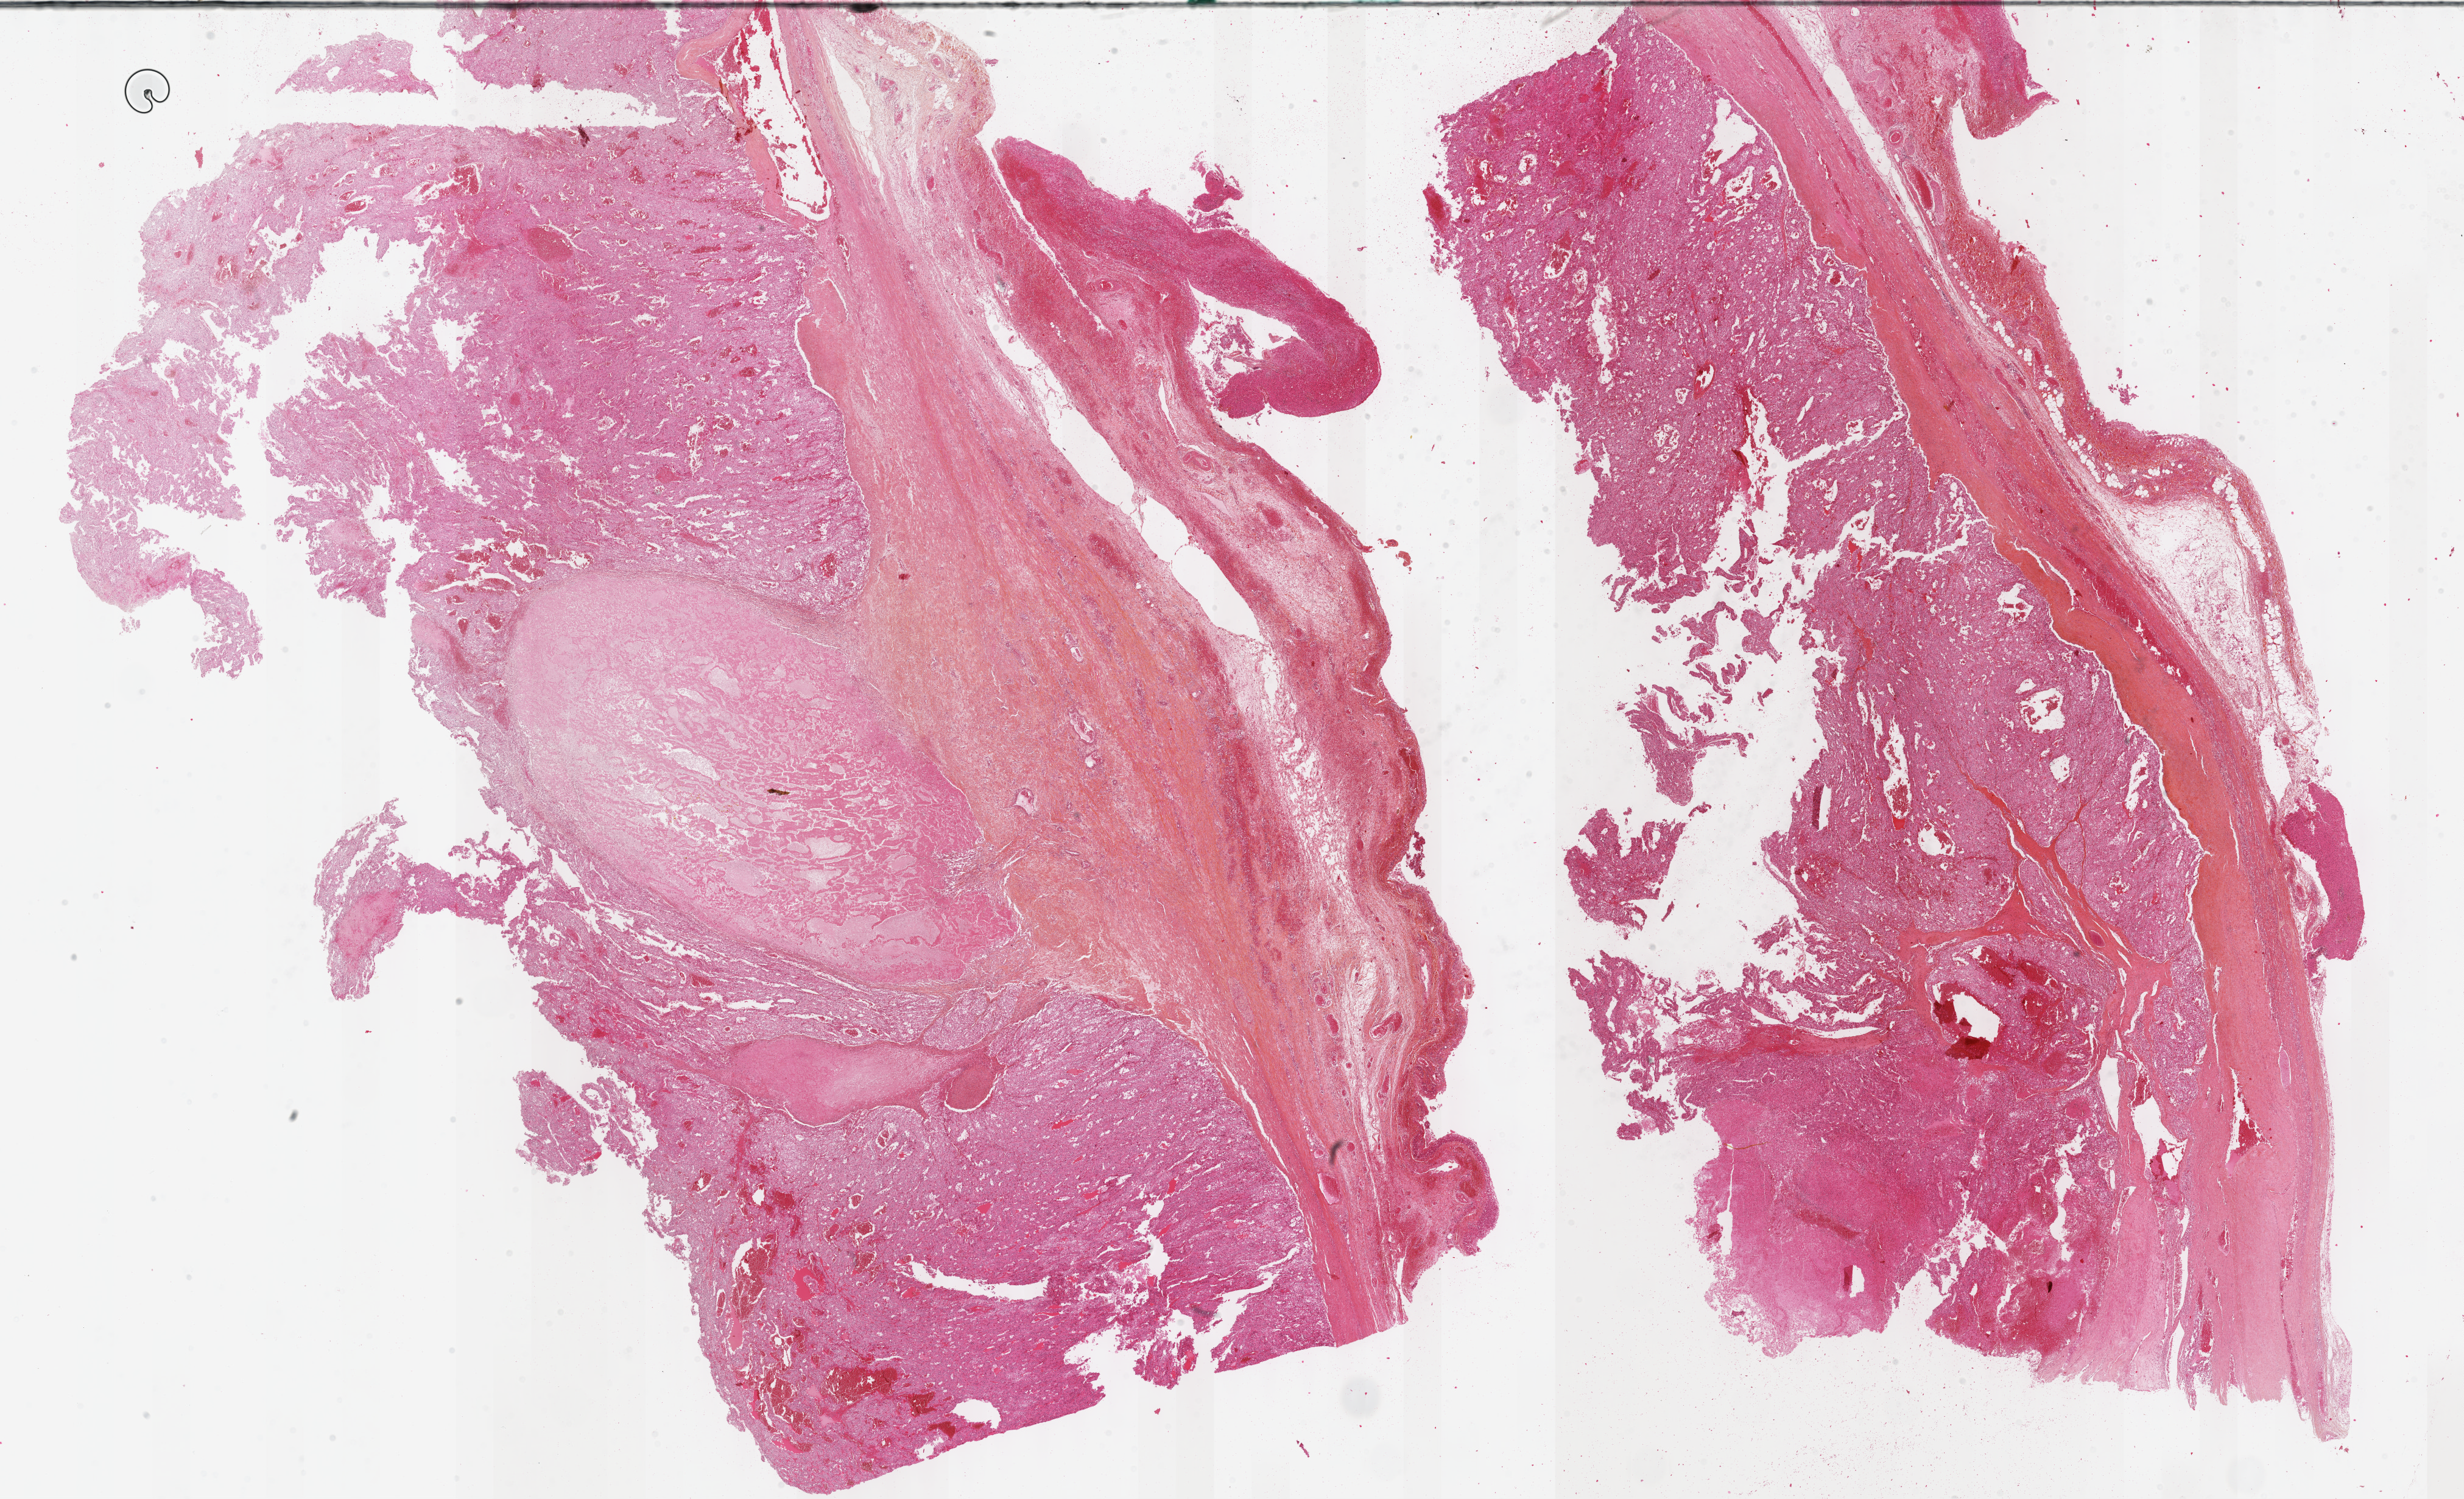
Digitized Hematoxylin and eosin (H&E) stained tissue section (whole slide), whole scanned area (about 32.7 x 19.9 mm, acquisition: 40x scan) shown as a low-resolution overview, formalin-fixed paraffin-embedded (FFPE) diagnostic section, sample: primary tumour, adrenal cortex. Female, age 34 years at initial diagnosis.
* pathologic diagnosis: Adrenal cortical carcinoma (cortex of adrenal gland)